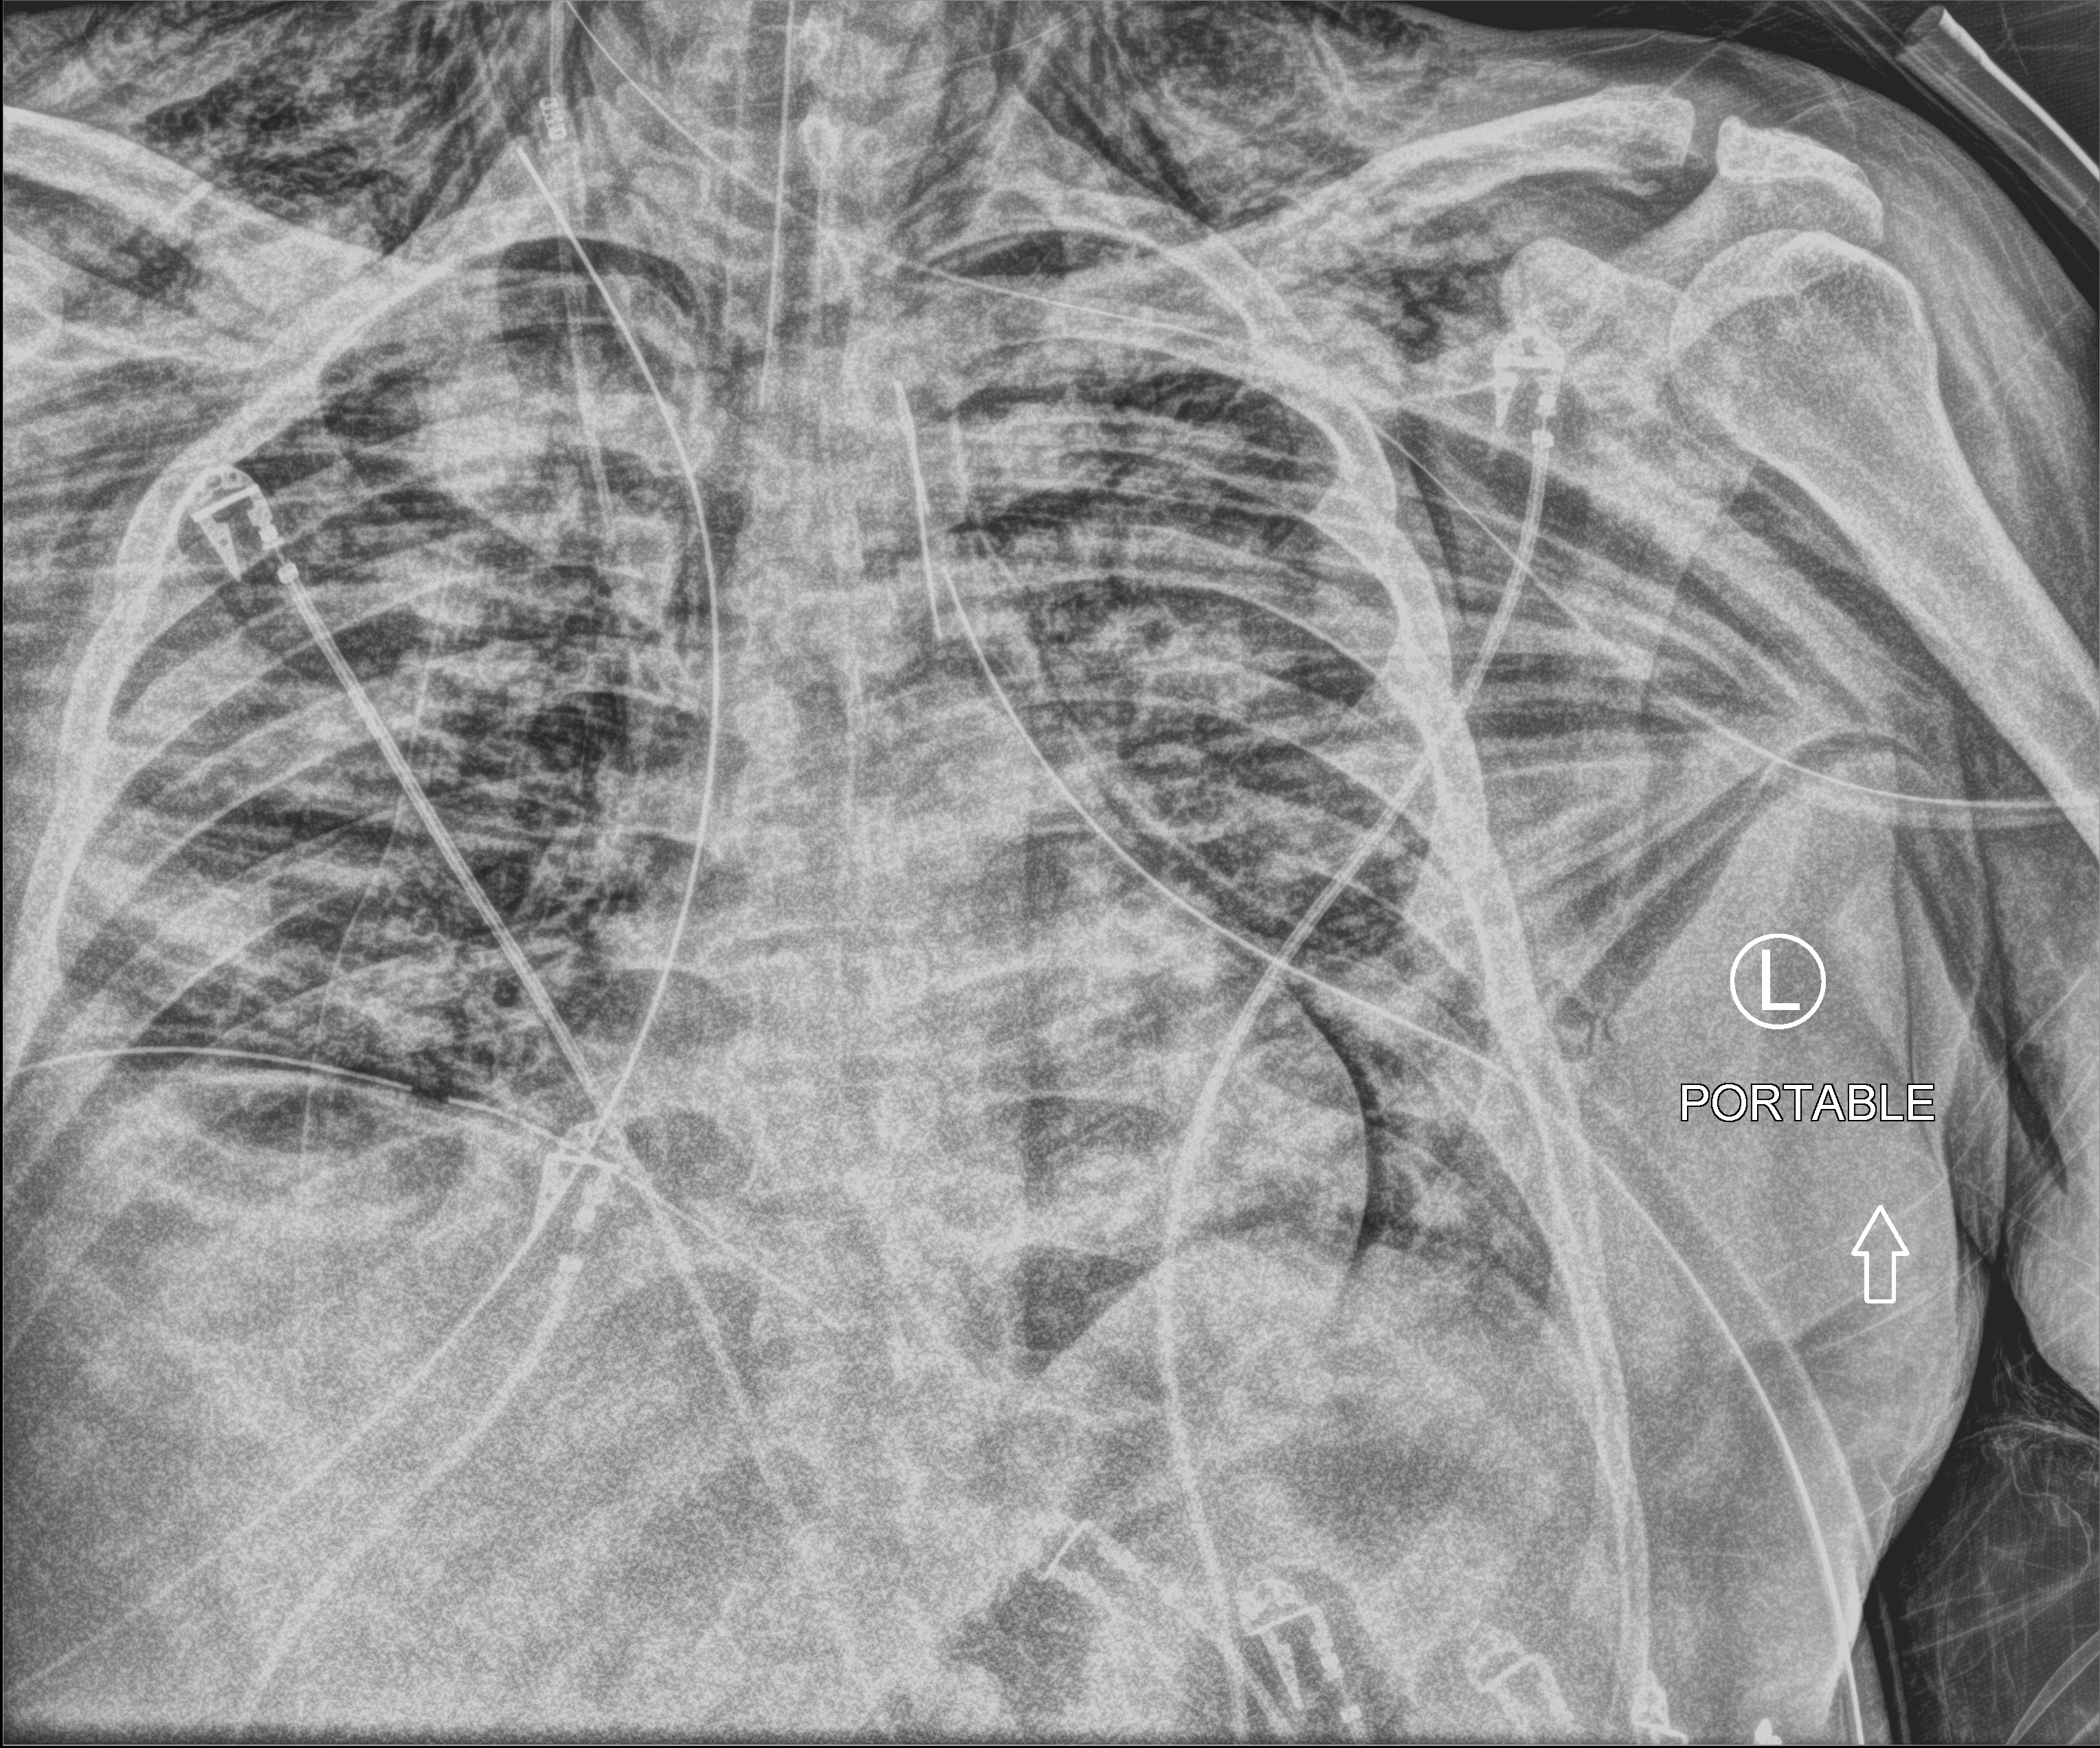
Bedside chest radiograph (computed radiography), anteroposterior (AP) projection. Patient hospitalised with COVID-19; male, aged 18–59 years.
Admission-level facts for this patient (not findings on this image; timing relative to this image not recorded): mechanically ventilated during this hospital stay: yes; admitted to intensive care during this hospital stay: yes.